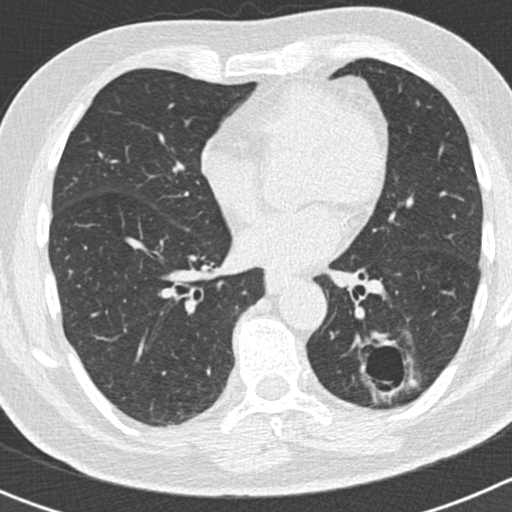
Chest CT (low-dose screening protocol), one axial image. Second screening round (one year after baseline). Lung window (W 1500 / L -600 HU). Standard (soft-tissue) reconstruction kernel (B30f). 512 × 512 image matrix. Male, age 66 years at enrolment.
Expert reader's lesion annotation, bounding box (x1, y1, x2, y2) in pixels: (349, 331, 414, 405). The exam's reader record, not a measurement of the box and not confirmed to be the same lesion: non-calcified nodule or mass ≥4 mm, left lower lobe, 50 × 33 mm, smooth margins, pre-existing on the prior screen: yes; interval growth: yes. Official screen result: positive, other. Lung cancer was diagnosed 440 days after this screen (after the third annual screen): adenocarcinoma, NOS, left lower lobe, poorly differentiated (G3), stage IB (AJCC 6th edition), 38 mm at pathology.